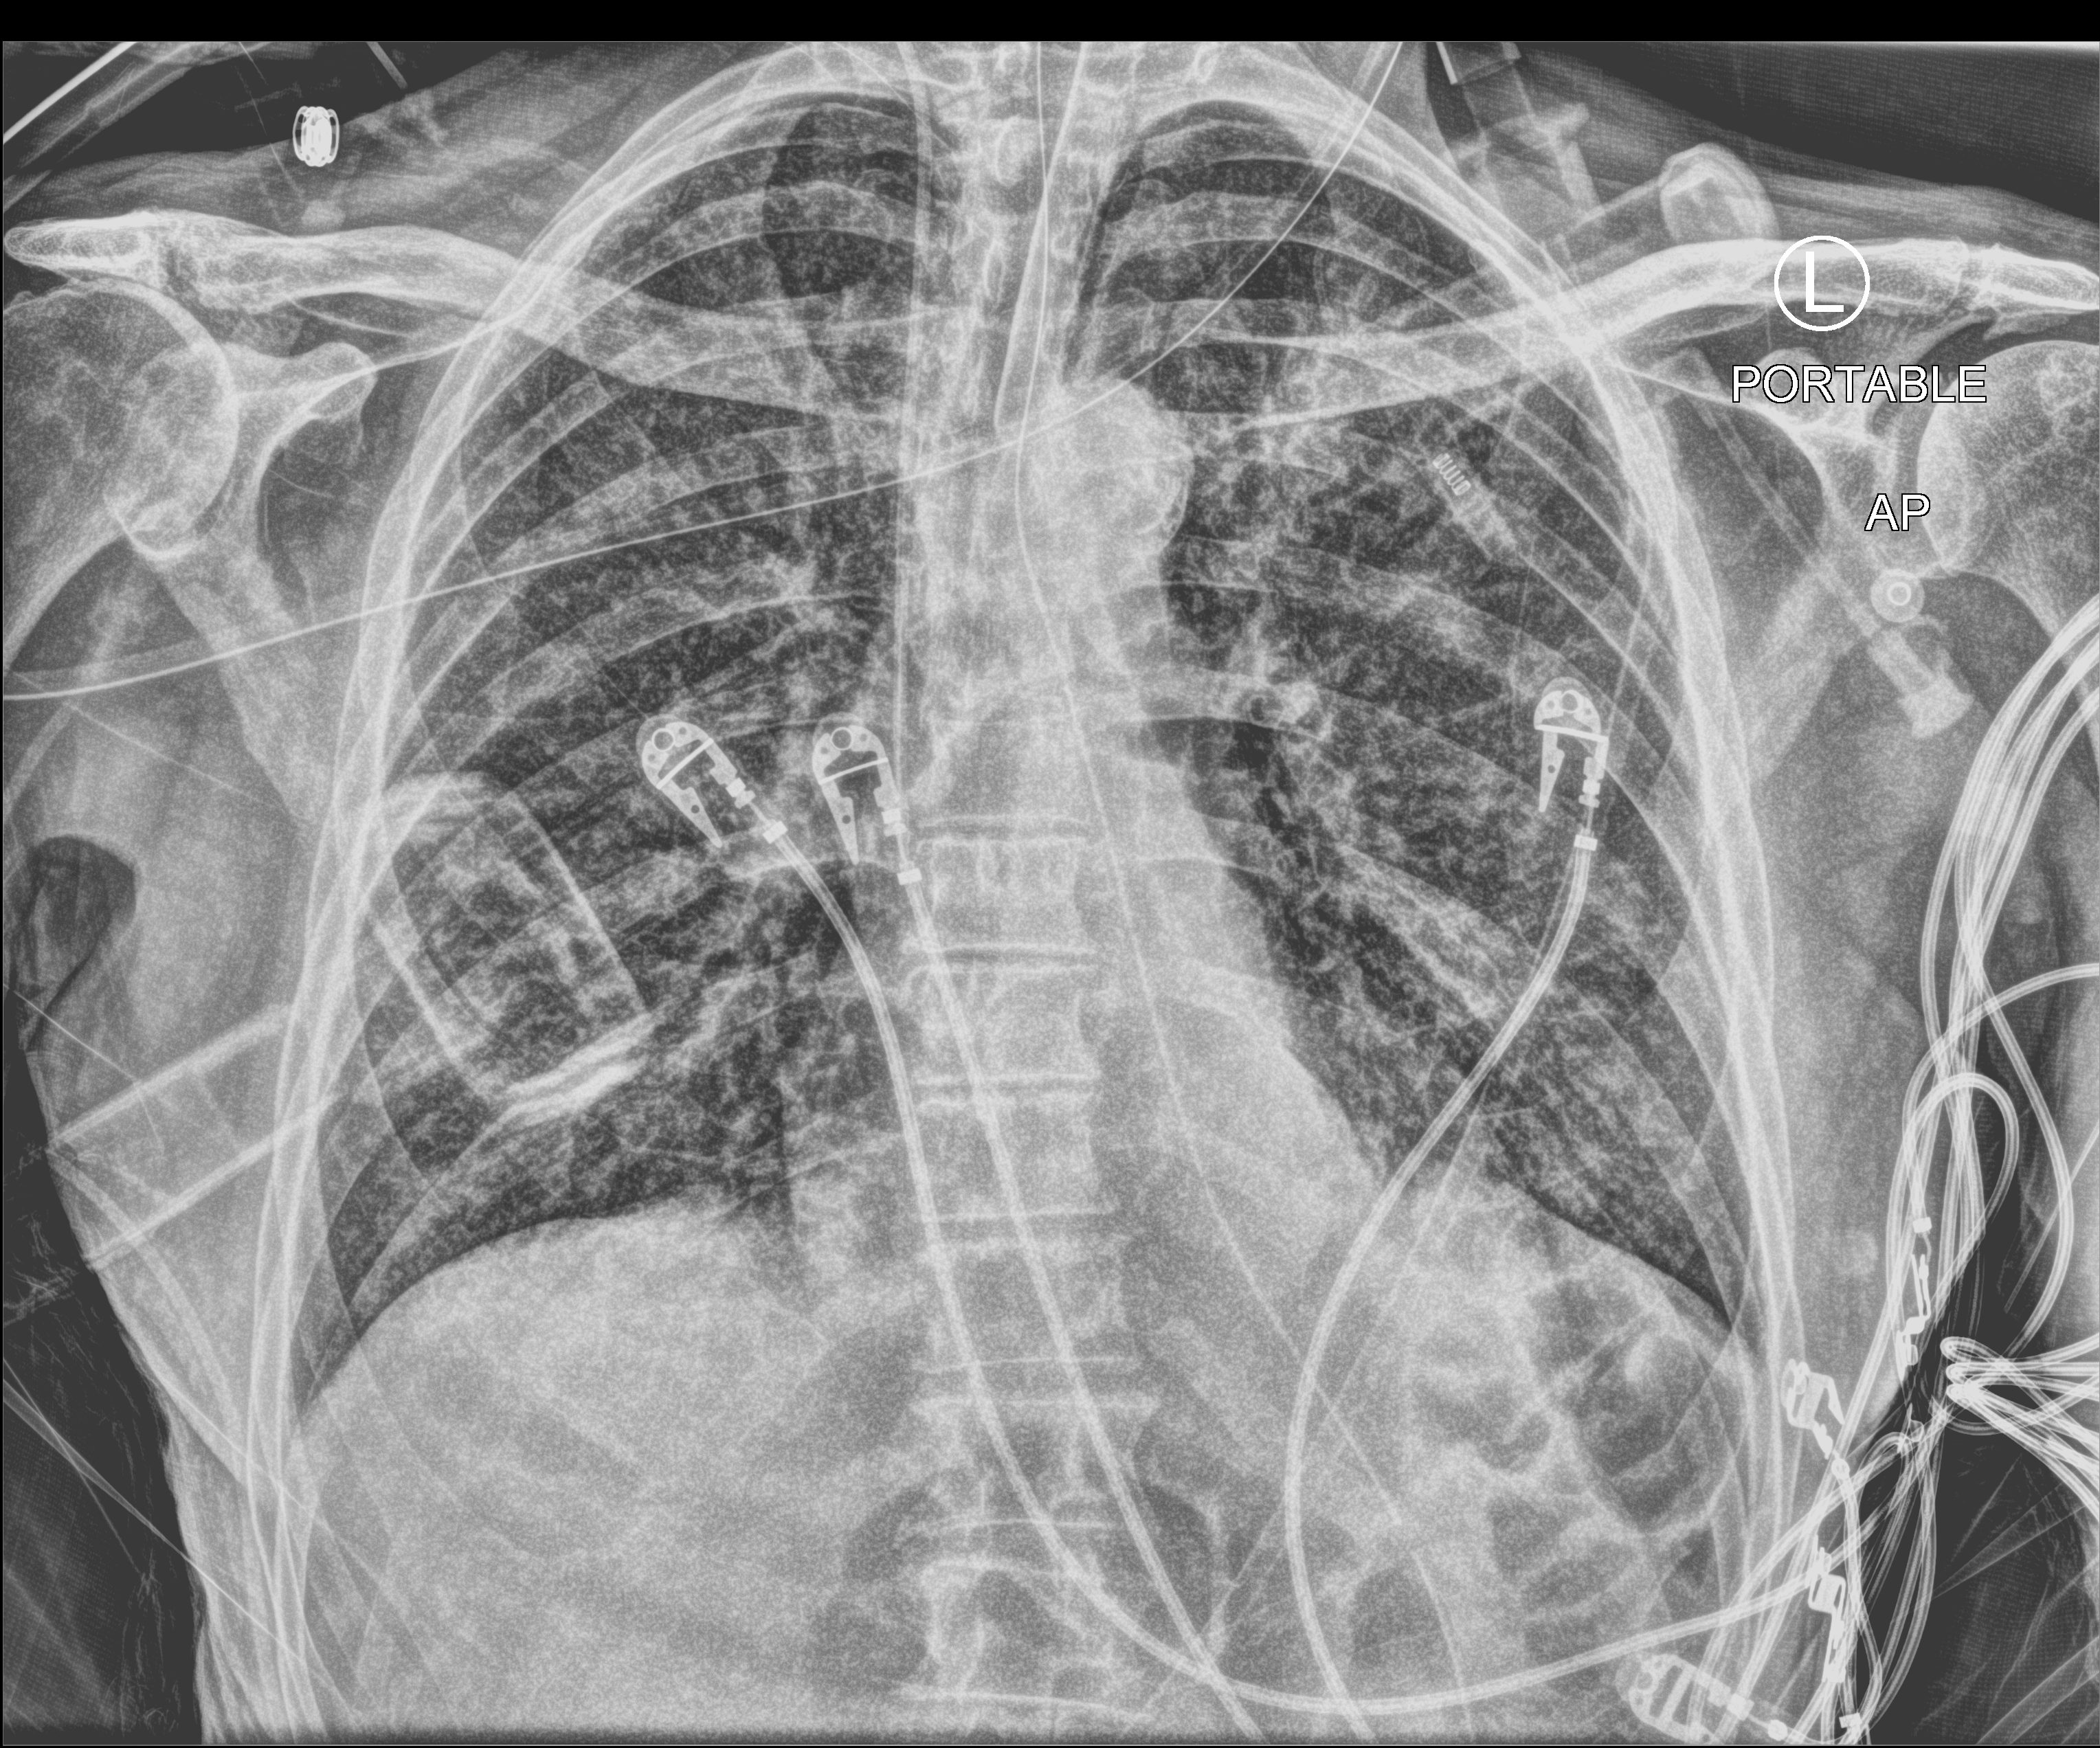
Bedside chest radiograph (computed radiography), anteroposterior (AP) projection. Patient hospitalised with COVID-19; male, aged 75–90 years.
From the hospital-stay record, not from the radiograph (when in the stay this image was taken is not recorded):
- mechanically ventilated during this hospital stay: yes
- admitted to intensive care during this hospital stay: yes